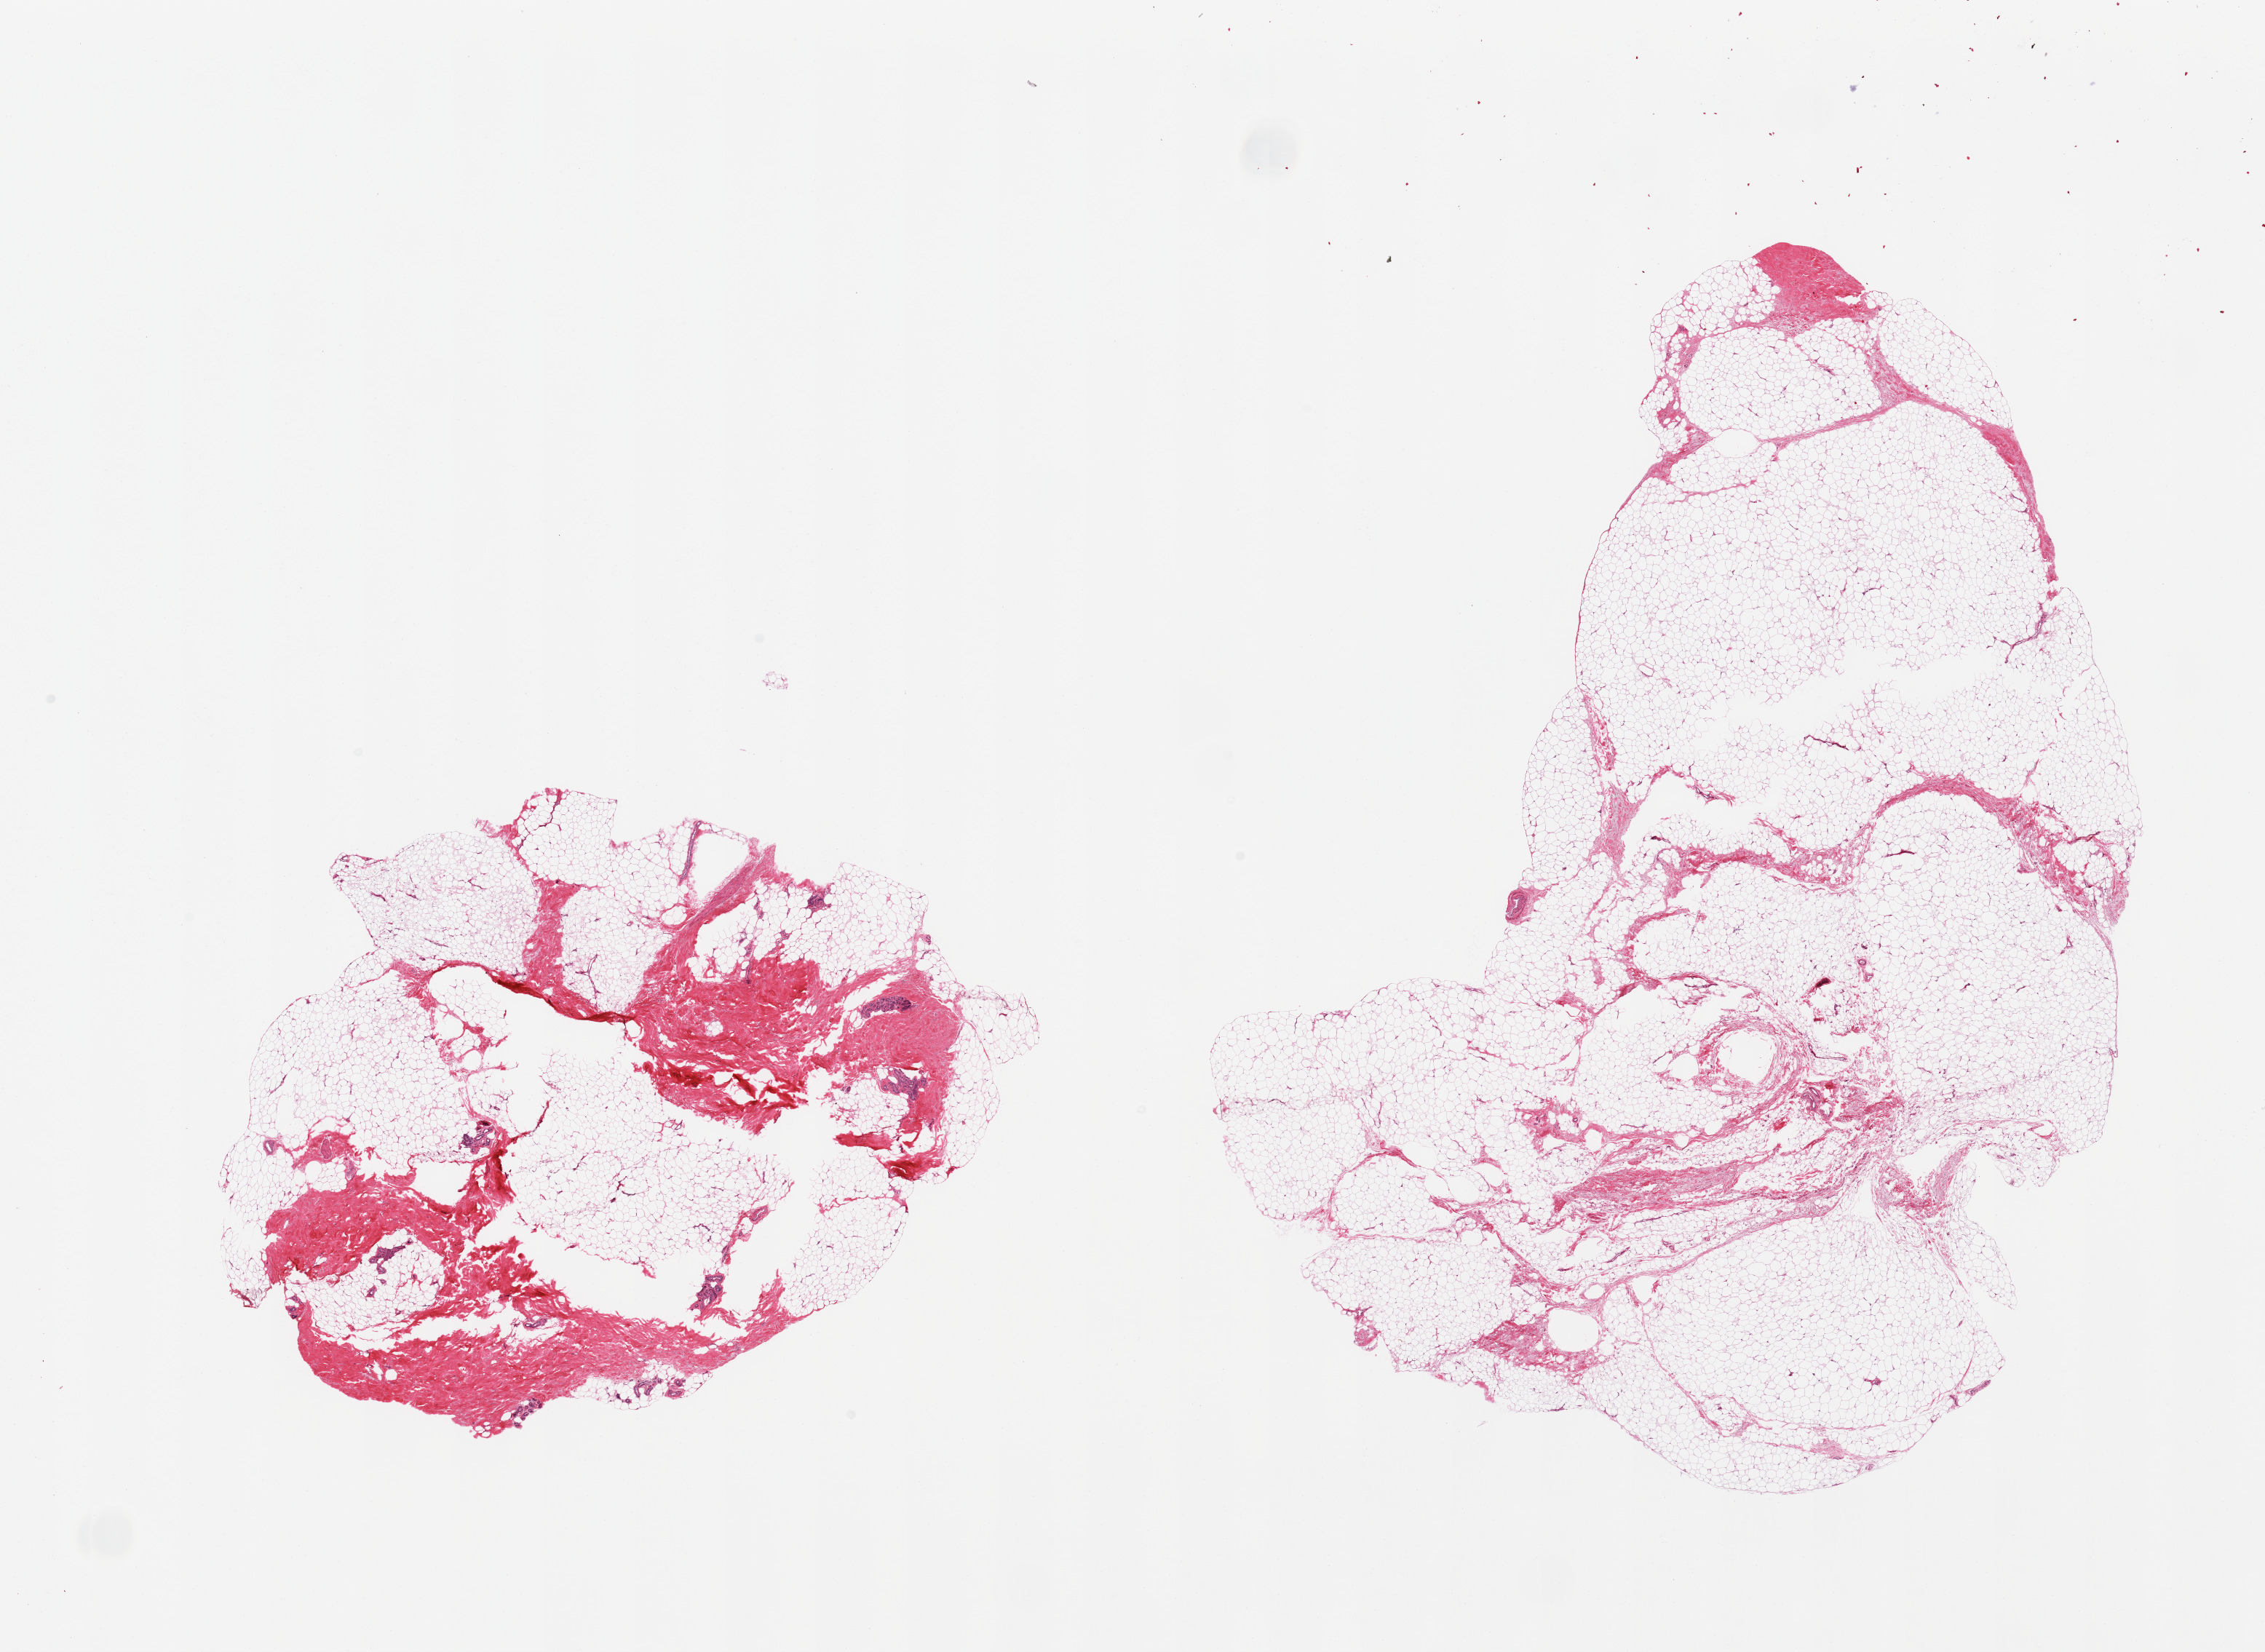
Digitized H&E-stained section, low-resolution overview of the scanned area, about 24.6 x 18.0 mm (slide scanned at 20x); PAXgene-fixed, paraffin-embedded tissue; target tissue: adipose tissue; tissue donor sample. Male donor.
Reviewer comment on this tissue sample: 2 pieces, fascia/vascular elements up to ~40% of tissue.